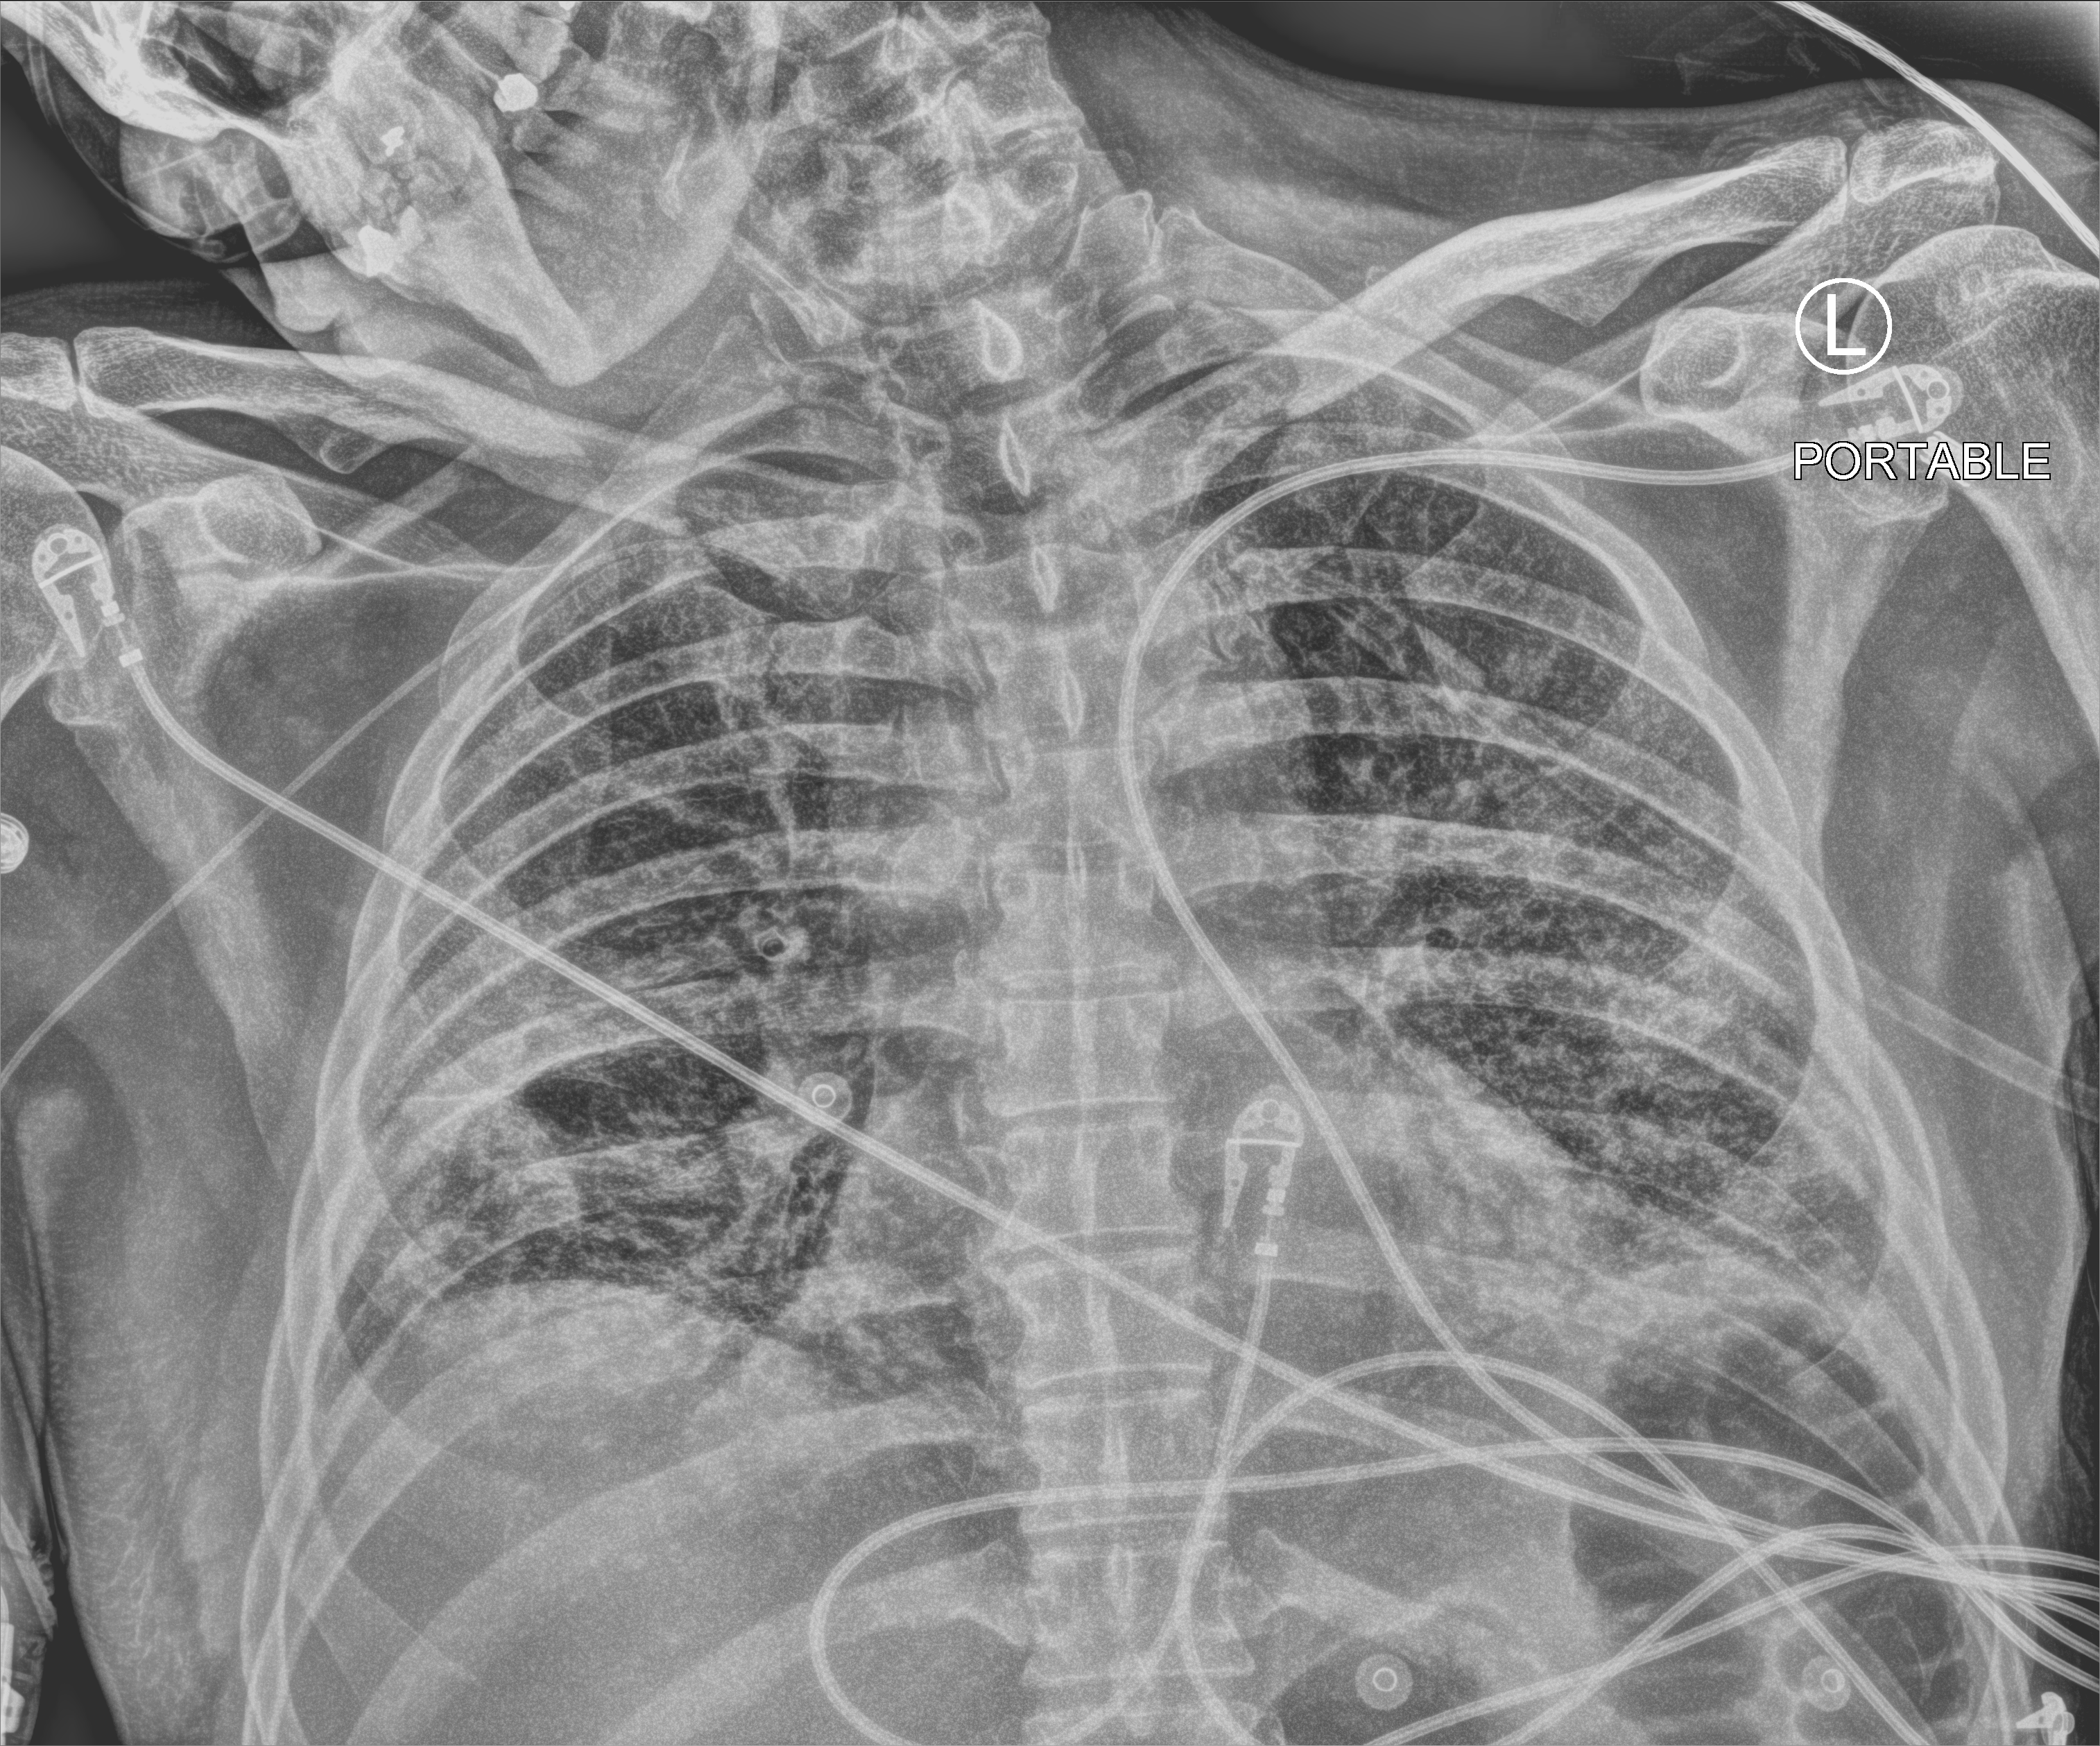
Chest X-ray (portable); anteroposterior (AP) projection. Male patient hospitalised with COVID-19, age 60–74 years.
From the hospital-stay record, not from the radiograph (when in the stay this image was taken is not recorded): admitted to intensive care during this hospital stay: yes; hypertension (admission record): no.